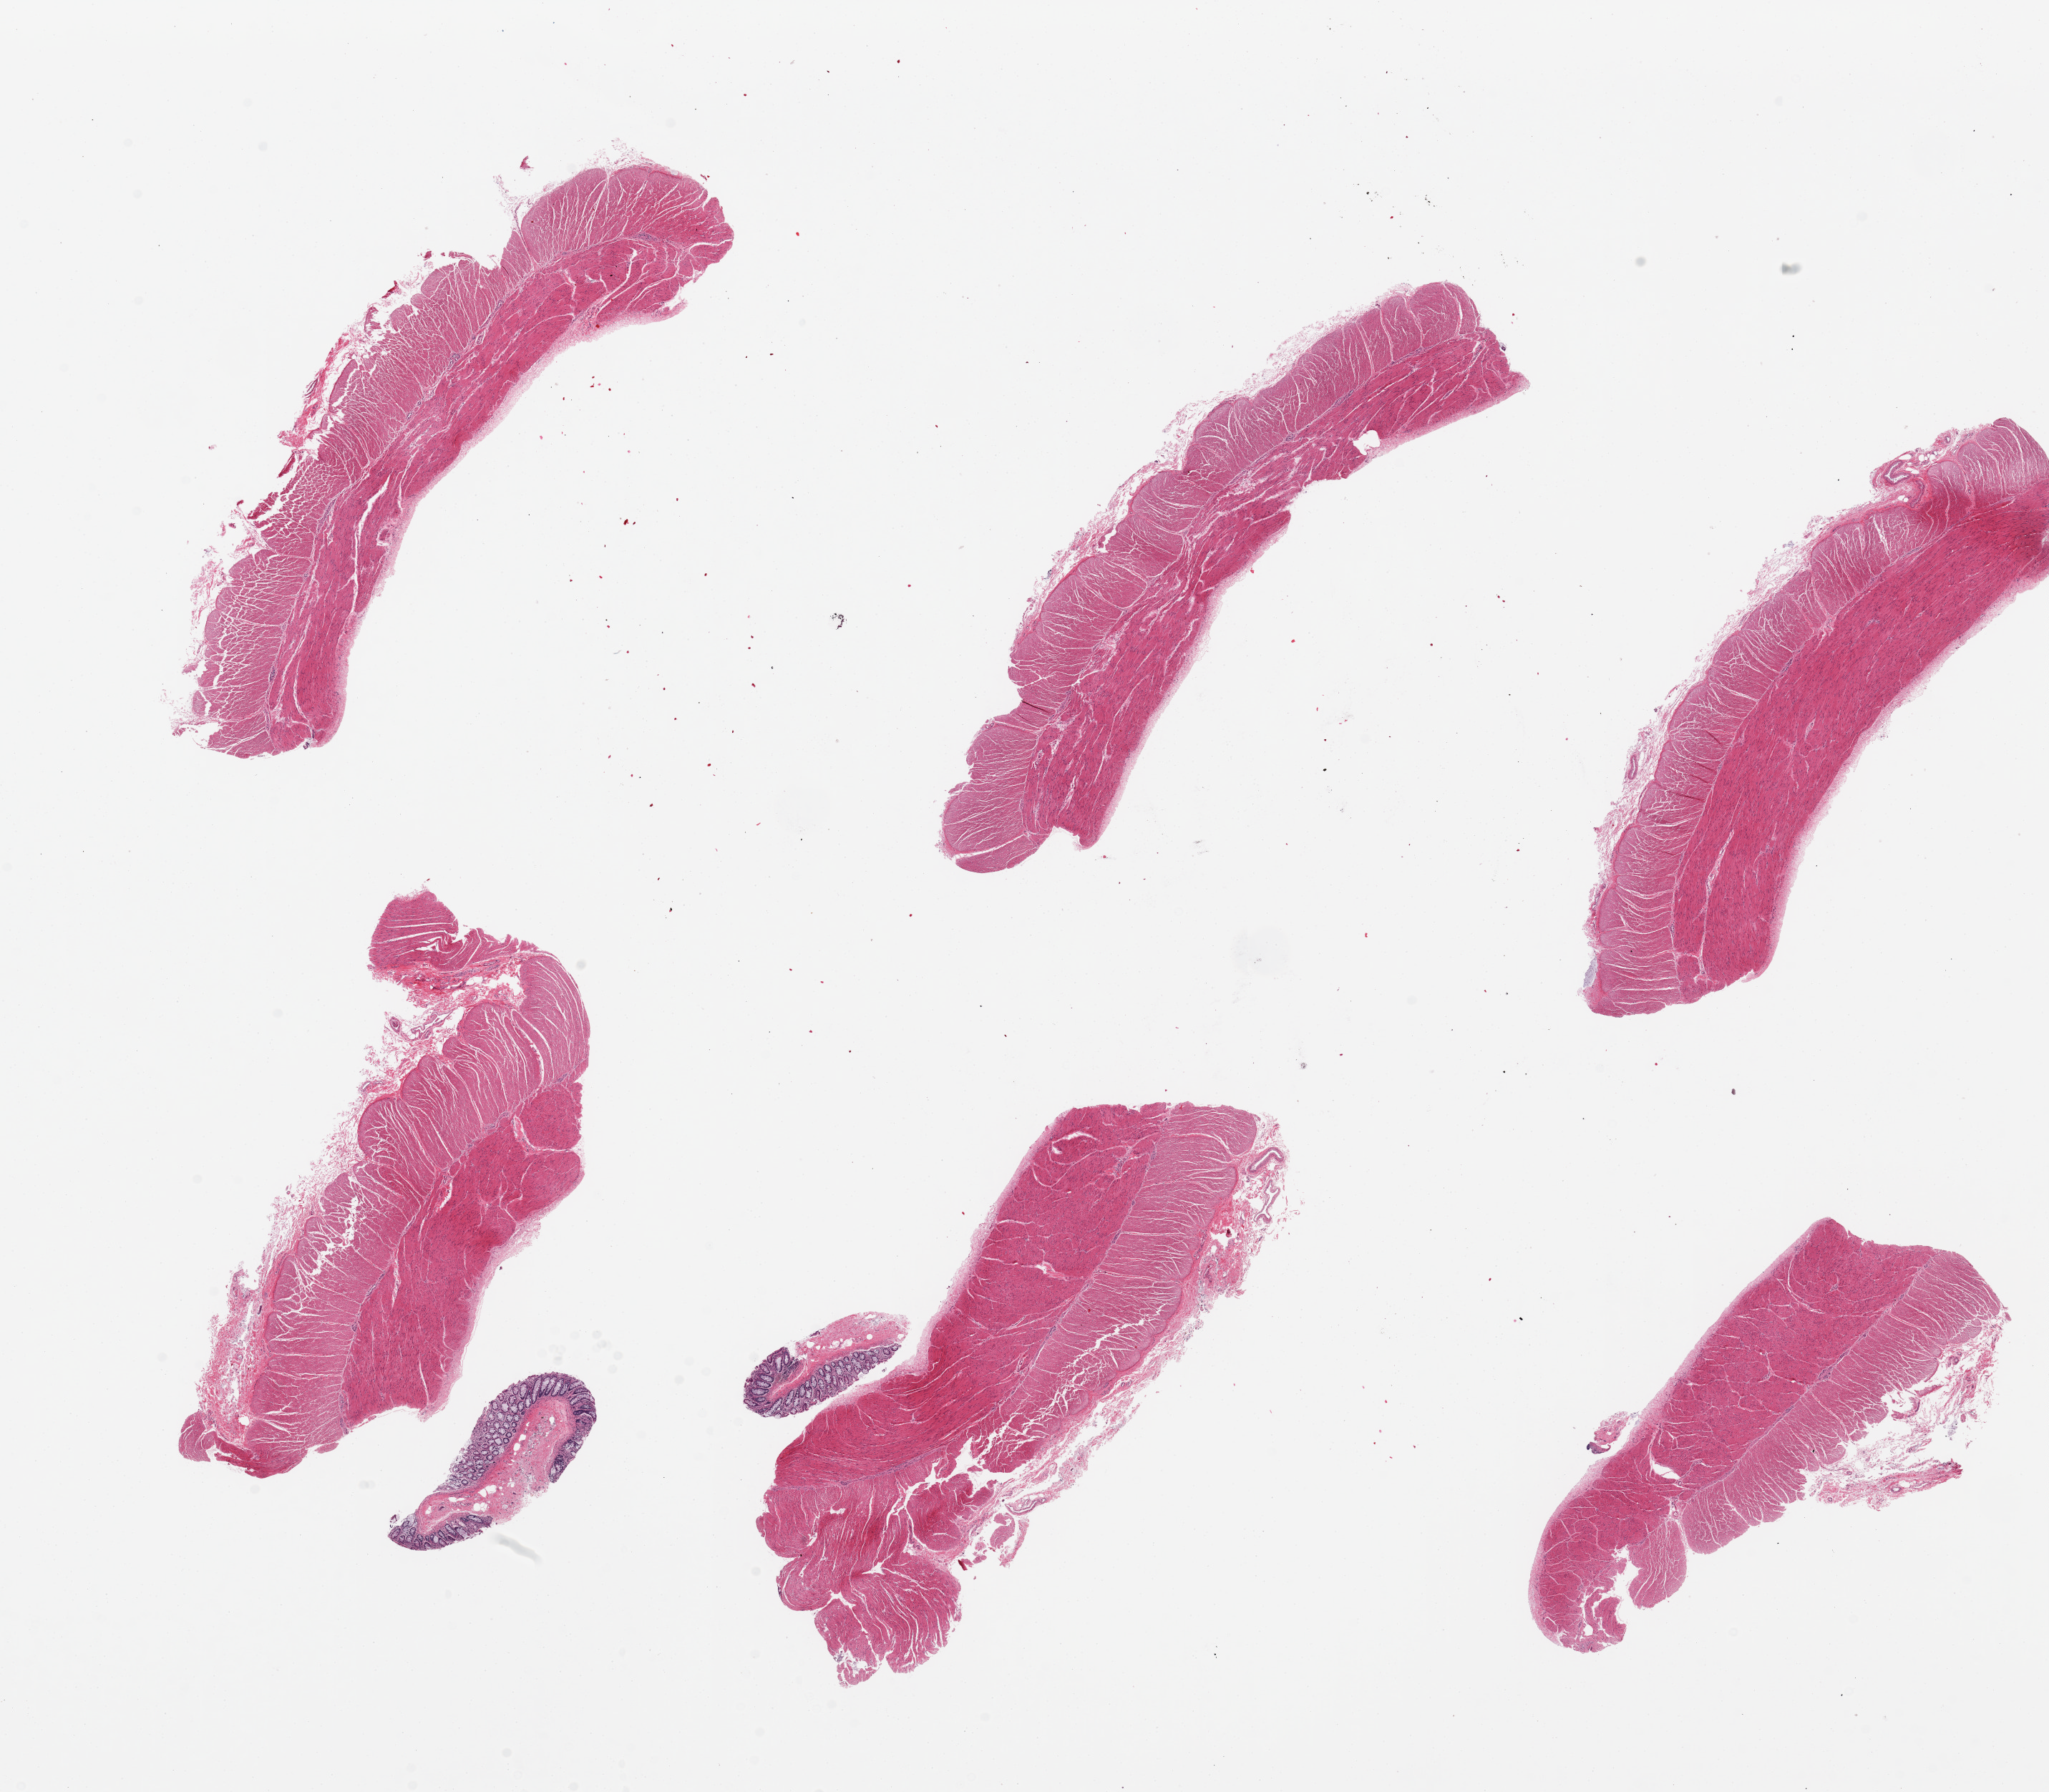
Hematoxylin and eosin (H&E) whole-slide image, low-resolution overview of the scanned area, about 22.6 x 19.8 mm (slide scanned at 20x), PAXgene-fixed, paraffin-embedded tissue, sampled site (target tissue): sigmoid colon, tissue donor sample. Donor: female.
Review note (as recorded): 6 pieces, up to 8x4mm; All have targeted muscularis.